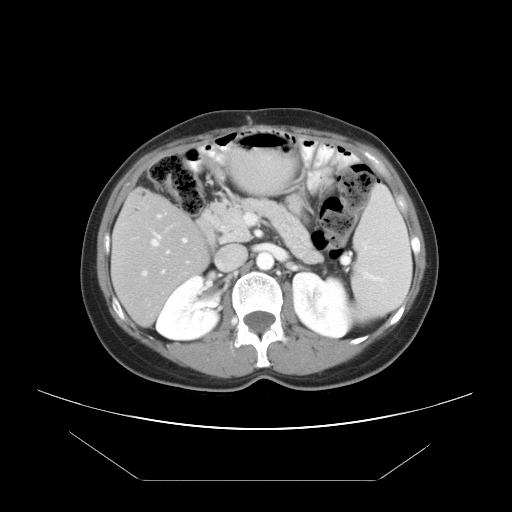
Contrast-enhanced abdominal CT, one axial slice. Slice 21 of 45 in the series (ordered by position). Intravenous contrast given. Soft-tissue window (W 400 / L 40 HU). 512 × 512 image matrix, field of view 405 × 405 mm. Female patient, age 52 years. Case-level facts recorded for this patient, not image findings: diagnosis: colorectal cancer liver metastases, imaged before liver resection; multiple liver metastases: yes; largest metastasis: 2.5 cm; disease in both lobes: no.
Outlined on this slice (outlined manually by an expert reader):
- hepatic veins: bounding box <143,234,165,276> (left, top, right, bottom; pixels)
- liver: <112,192,207,324>
- planned liver remnant (the part of the liver to remain after resection): <112,192,206,324>
- portal vein (with intrahepatic branches): <156,214,188,254>